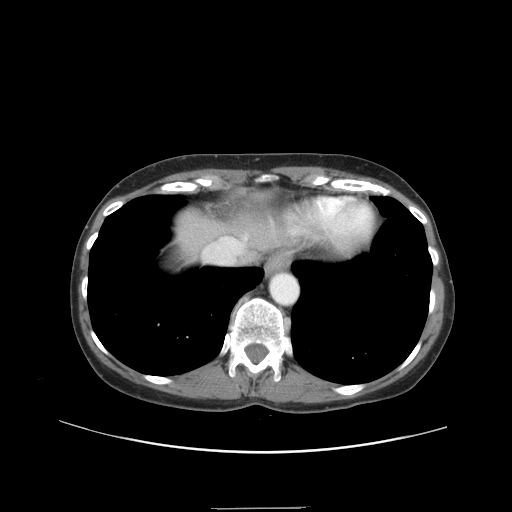
Contrast-enhanced abdominal CT, one axial slice. Position 34 of 38 along the scan axis. Soft-tissue window (W 400 / L 40 HU). 5 mm slice thickness. 512 × 512 image matrix, field of view 388 × 388 mm. Female patient, age 64 years. From the clinical record (not read from this slice): diagnosis: colorectal cancer liver metastases, imaged before liver resection; multiple liver metastases: no.
Outlined on this slice (outlined manually by an expert reader):
- hepatic veins: bounding box [x1, y1, x2, y2] px = [203, 236, 247, 264]
- liver: [181, 214, 220, 252]
- planned liver remnant (the part of the liver to remain after resection): [183, 214, 220, 236]